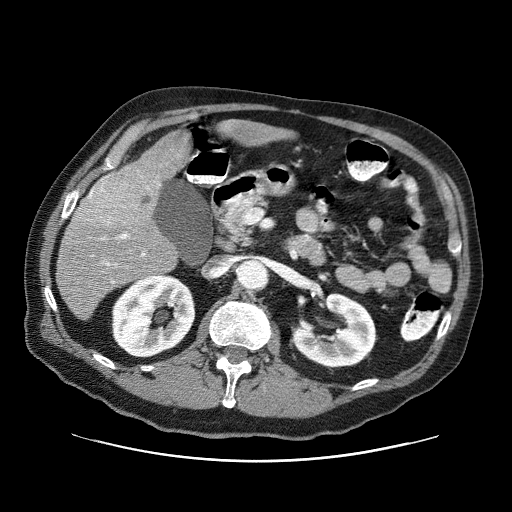
Contrast-enhanced abdominal CT (liver protocol), one axial slice. Position 29 of 87 along the scan axis. One of 3 acquisitions stored at this slice position. Soft-tissue window (W 400 / L 40 HU). 2.5 mm slice thickness. 512 × 512 image matrix, field of view 400 × 400 mm. From the clinical record (not read from this slice): diagnosis: hepatocellular carcinoma (patient treated with transarterial chemoembolisation; whether this scan precedes or follows treatment is not stated here); TNM stage (as recorded): Stage-IIIA; Child-Pugh class: A.
Structures marked on this image (semi-automatic segmentation, software-assisted and operator-edited):
- liver parenchyma outside the tumour (the mass and vessels are separate outlines, so this box may not span the whole liver): bounding box [x1, y1, x2, y2] px = [56, 120, 254, 321]
- mass: [72, 166, 160, 232]
- liver vessels: [89, 192, 145, 283]